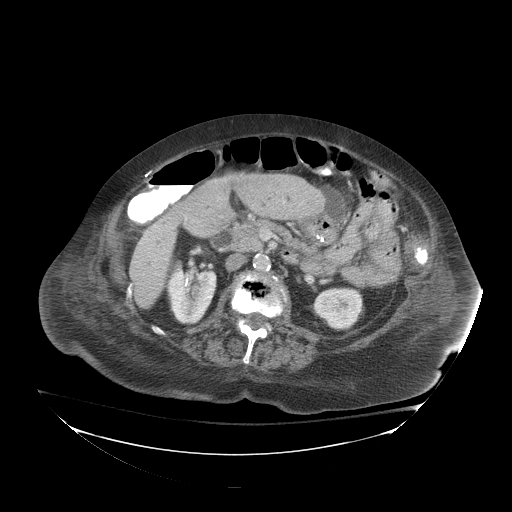
Contrast-enhanced abdominal CT (liver protocol), one axial slice; position 29 of 81 along the scan axis; 140 kVp; soft-tissue window (W 400 / L 40 HU); 2.5 mm slice thickness; 512 × 512 image matrix, field of view 500 × 500 mm. Case-level facts recorded for this patient, not image findings: diagnosis: hepatocellular carcinoma (patient treated with transarterial chemoembolisation; whether this scan precedes or follows treatment is not stated here); TNM stage (as recorded): Stage-I; Child-Pugh class: B; tumour differentiation: well-moderately differentiated; tumour nodularity: uninodular.
Annotated regions visible in this slice (semi-automatic segmentation, software-assisted and operator-edited):
- liver parenchyma outside the tumour (the mass and vessels are separate outlines, so this box may not span the whole liver): box from (x=128, y=216) to (x=176, y=308) px